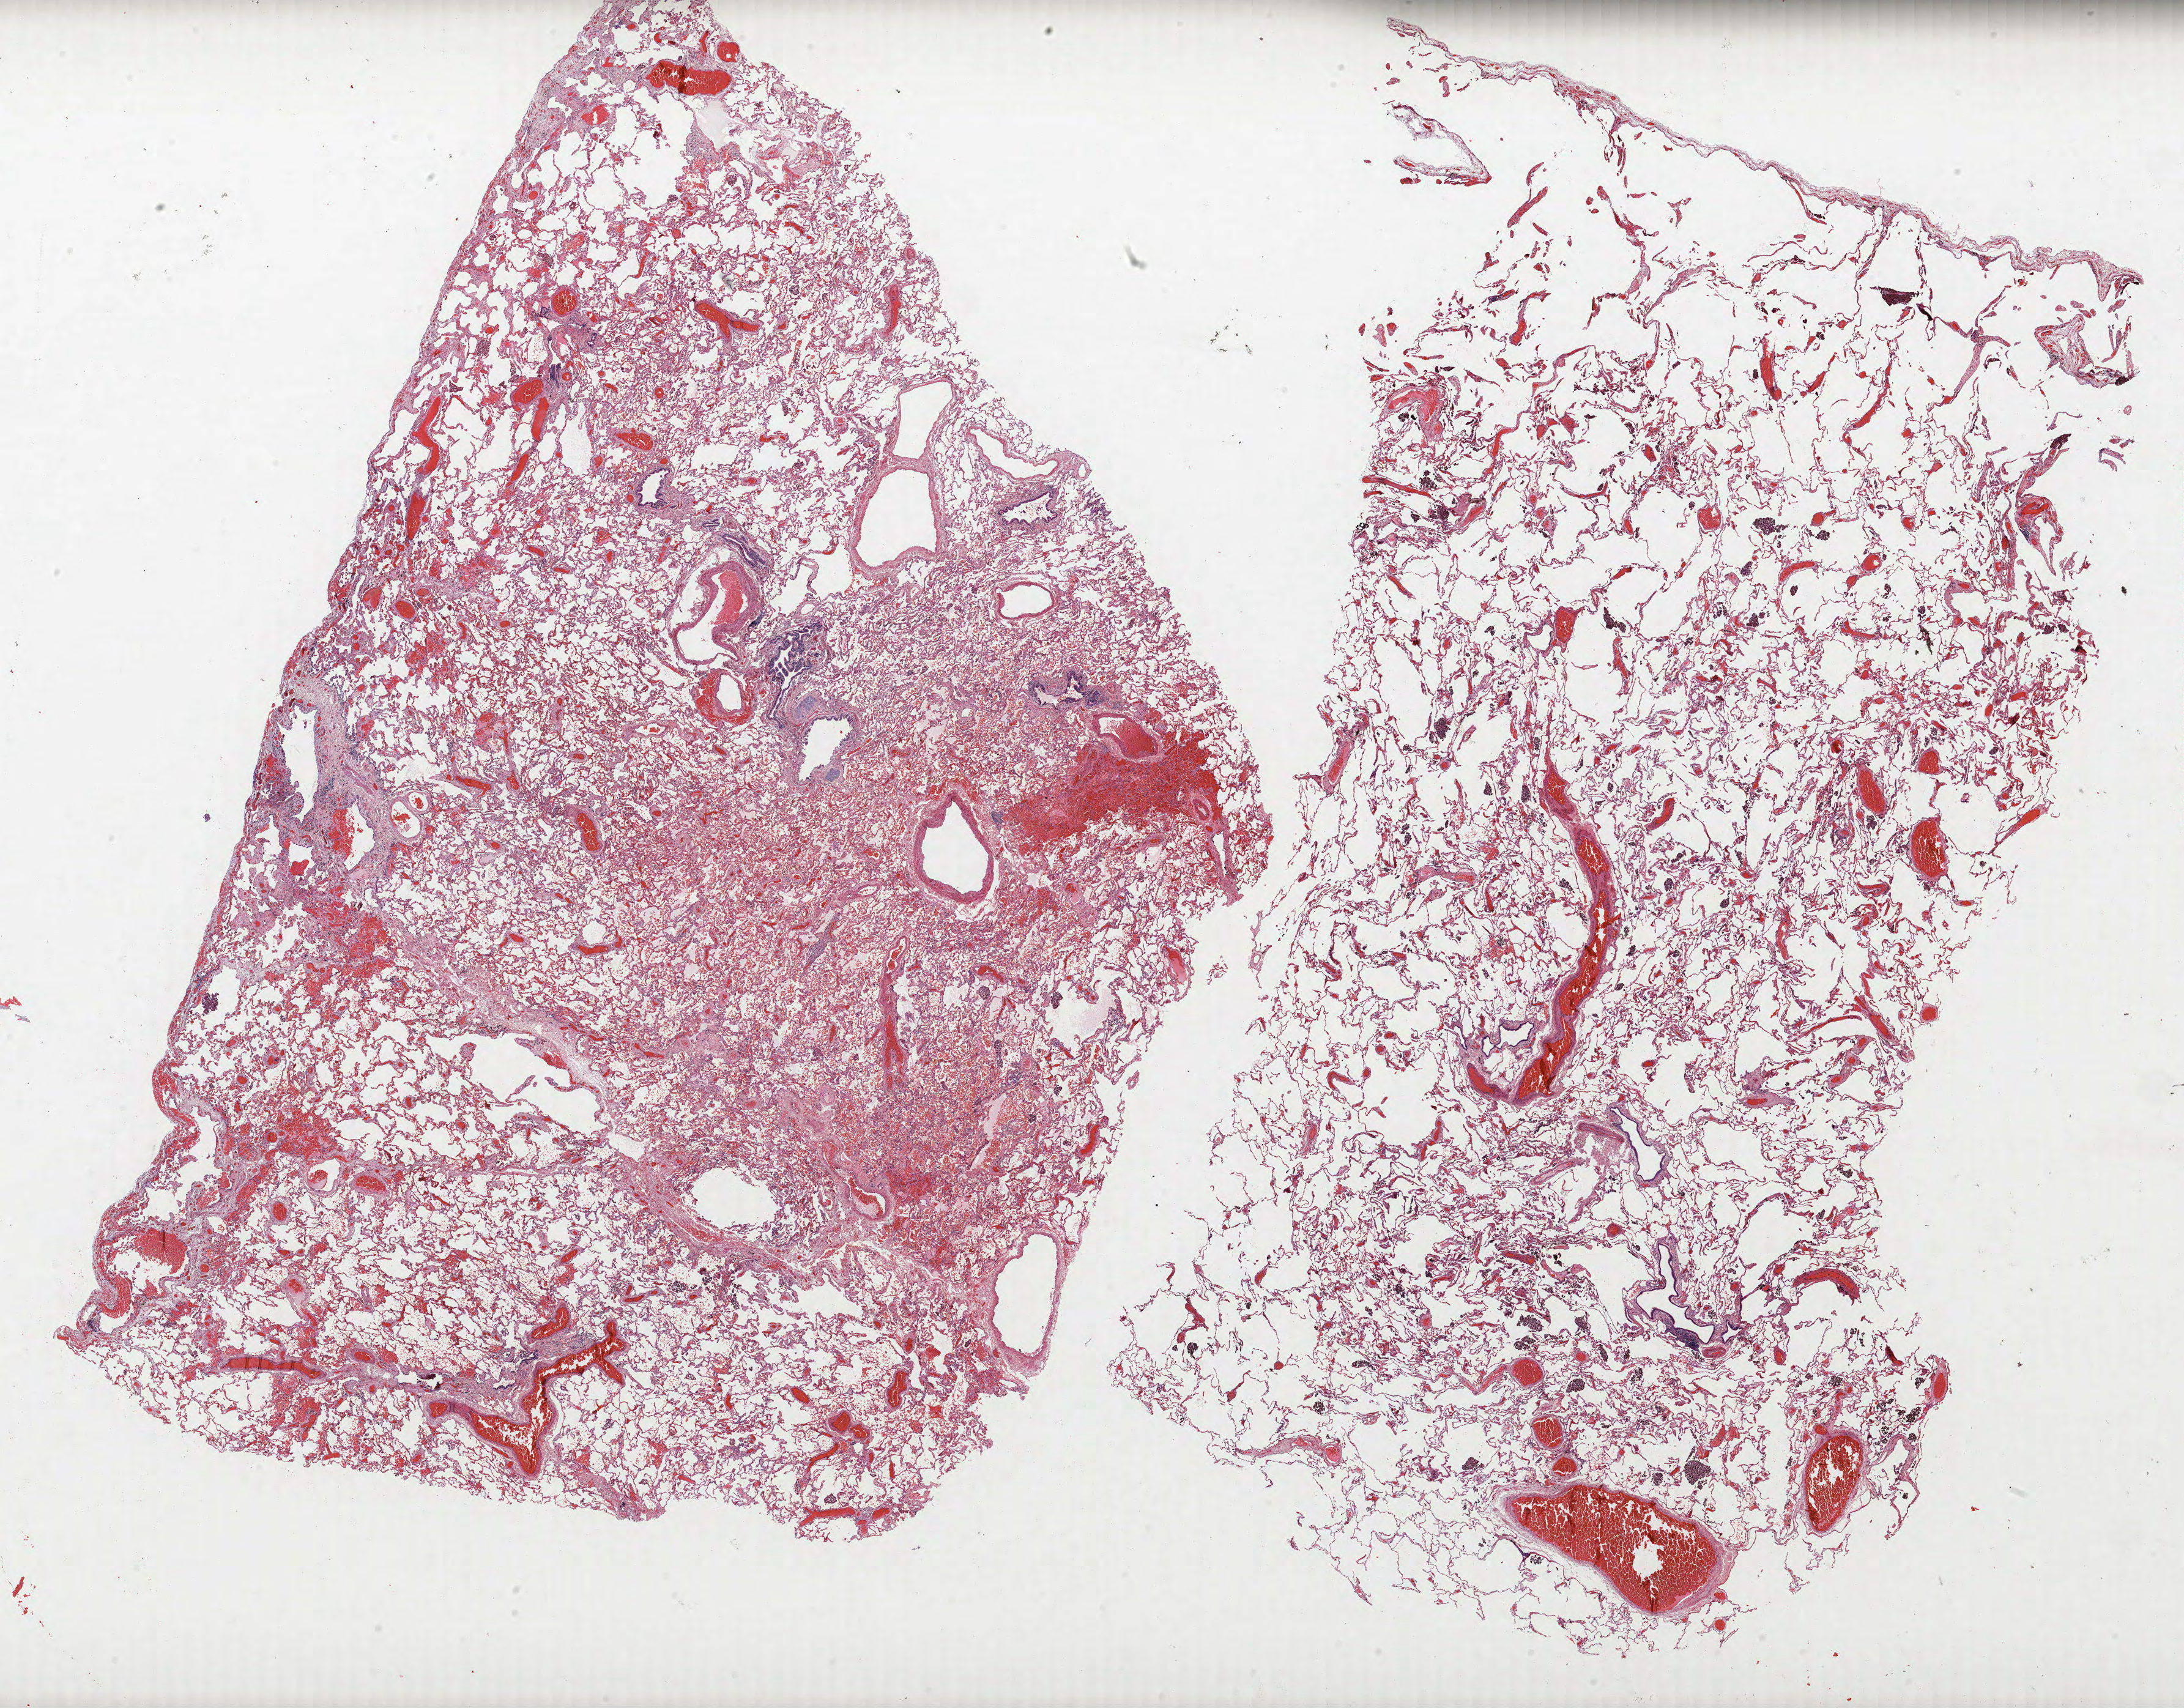
Hematoxylin and eosin (H&E) stained whole-slide image — whole scanned area (about 28.6 x 22.3 mm, from a 40x scan) shown as a low-resolution overview; formalin-fixed paraffin-embedded (FFPE) section; lung. Male, age 70 at enrolment. Former smoker at enrolment. Grade: poorly differentiated (G3).
• primary tumour location (clinical record): right upper lobe
• stage (AJCC 6th edition): IIIA
• participant's lung-cancer diagnosis: Adenocarcinoma, NOS
• tumour size (pathology): 50 mm